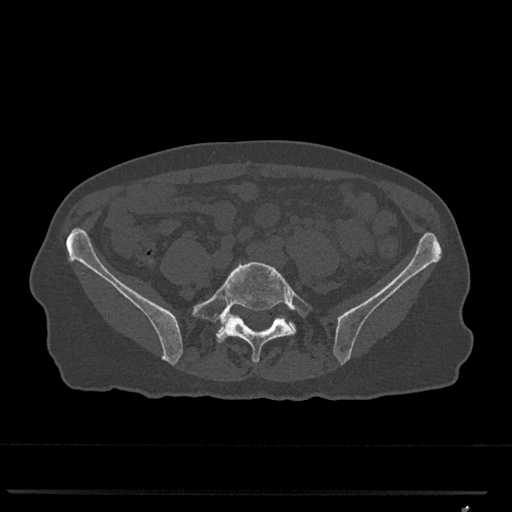
CT including the spine, one axial slice. Slice 148 of 793 in the series (ordered by position). Reconstruction kernel Br40s/3. Bone window (W 1800 / L 400 HU). 512 × 512 image matrix, field of view 380 × 380 mm. Patient: female, 62 years. Case-level facts recorded for this patient, not image findings: primary cancer: renal.
Outlined on this slice (semi-automatically segmented with operator editing):
- L5 vertebra: bounding box <192,261,313,362> (left, top, right, bottom; pixels)